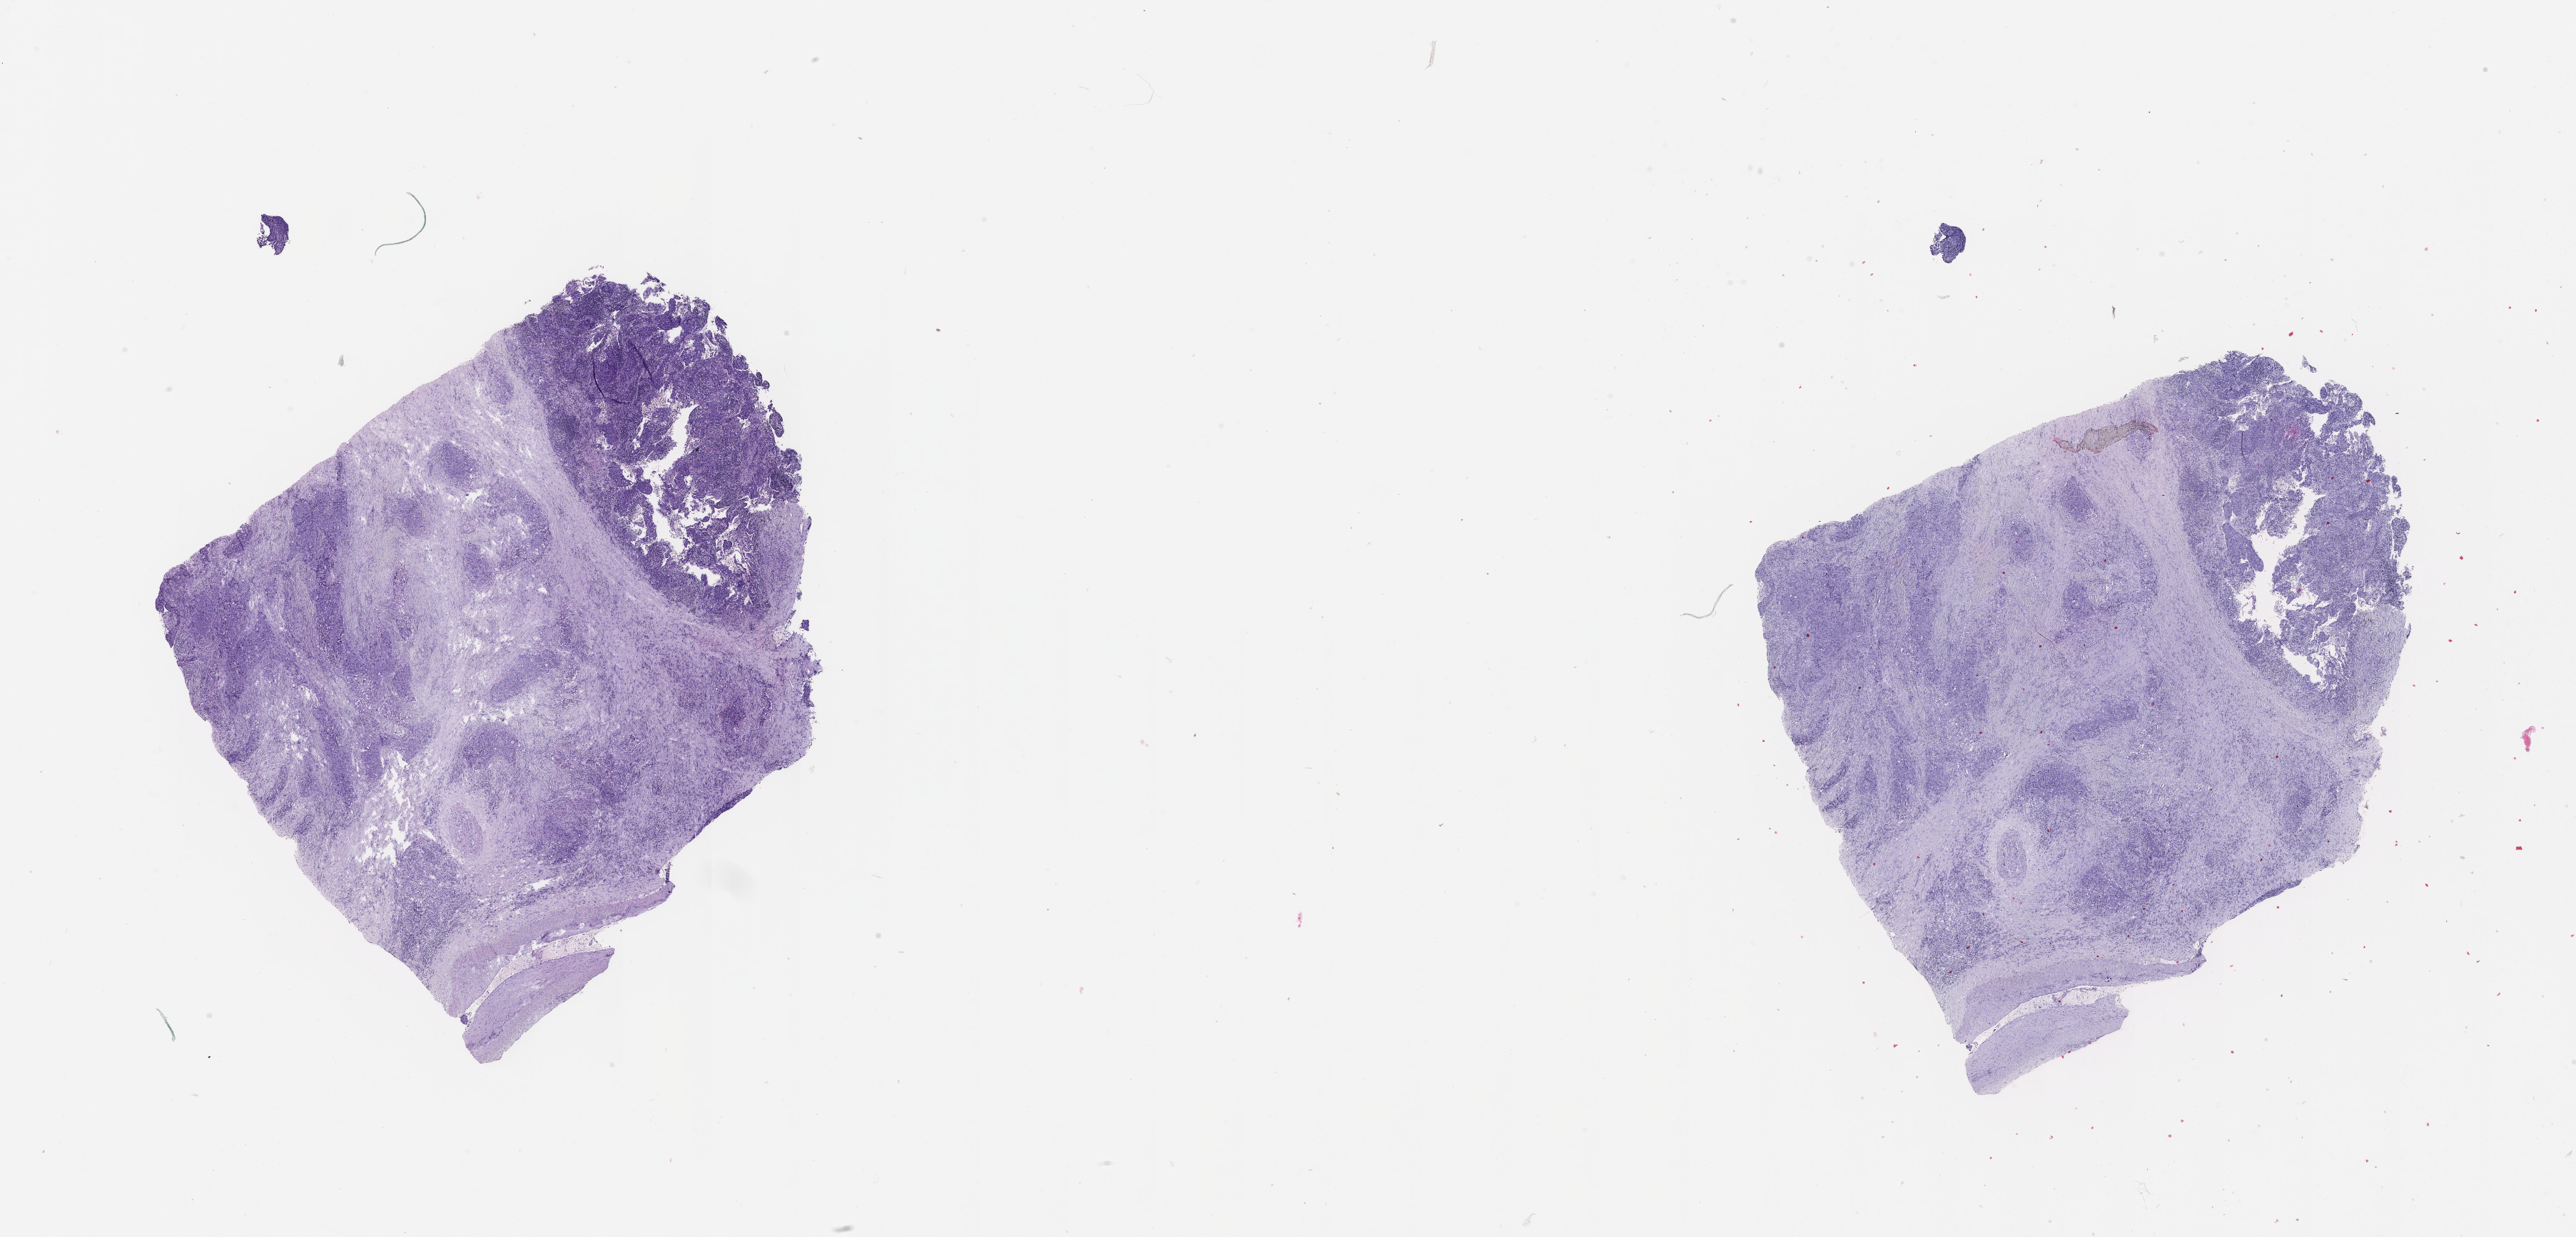
Whole-slide histology image, H&E-stained — shown as a low-resolution overview of the whole scanned area (about 29.1 x 14.0 mm, from a 20x scan), tumour tissue sample, lung. Patient: male, age 63 years.
Patient diagnosis (cohort enrolment): squamous cell carcinoma (lung).